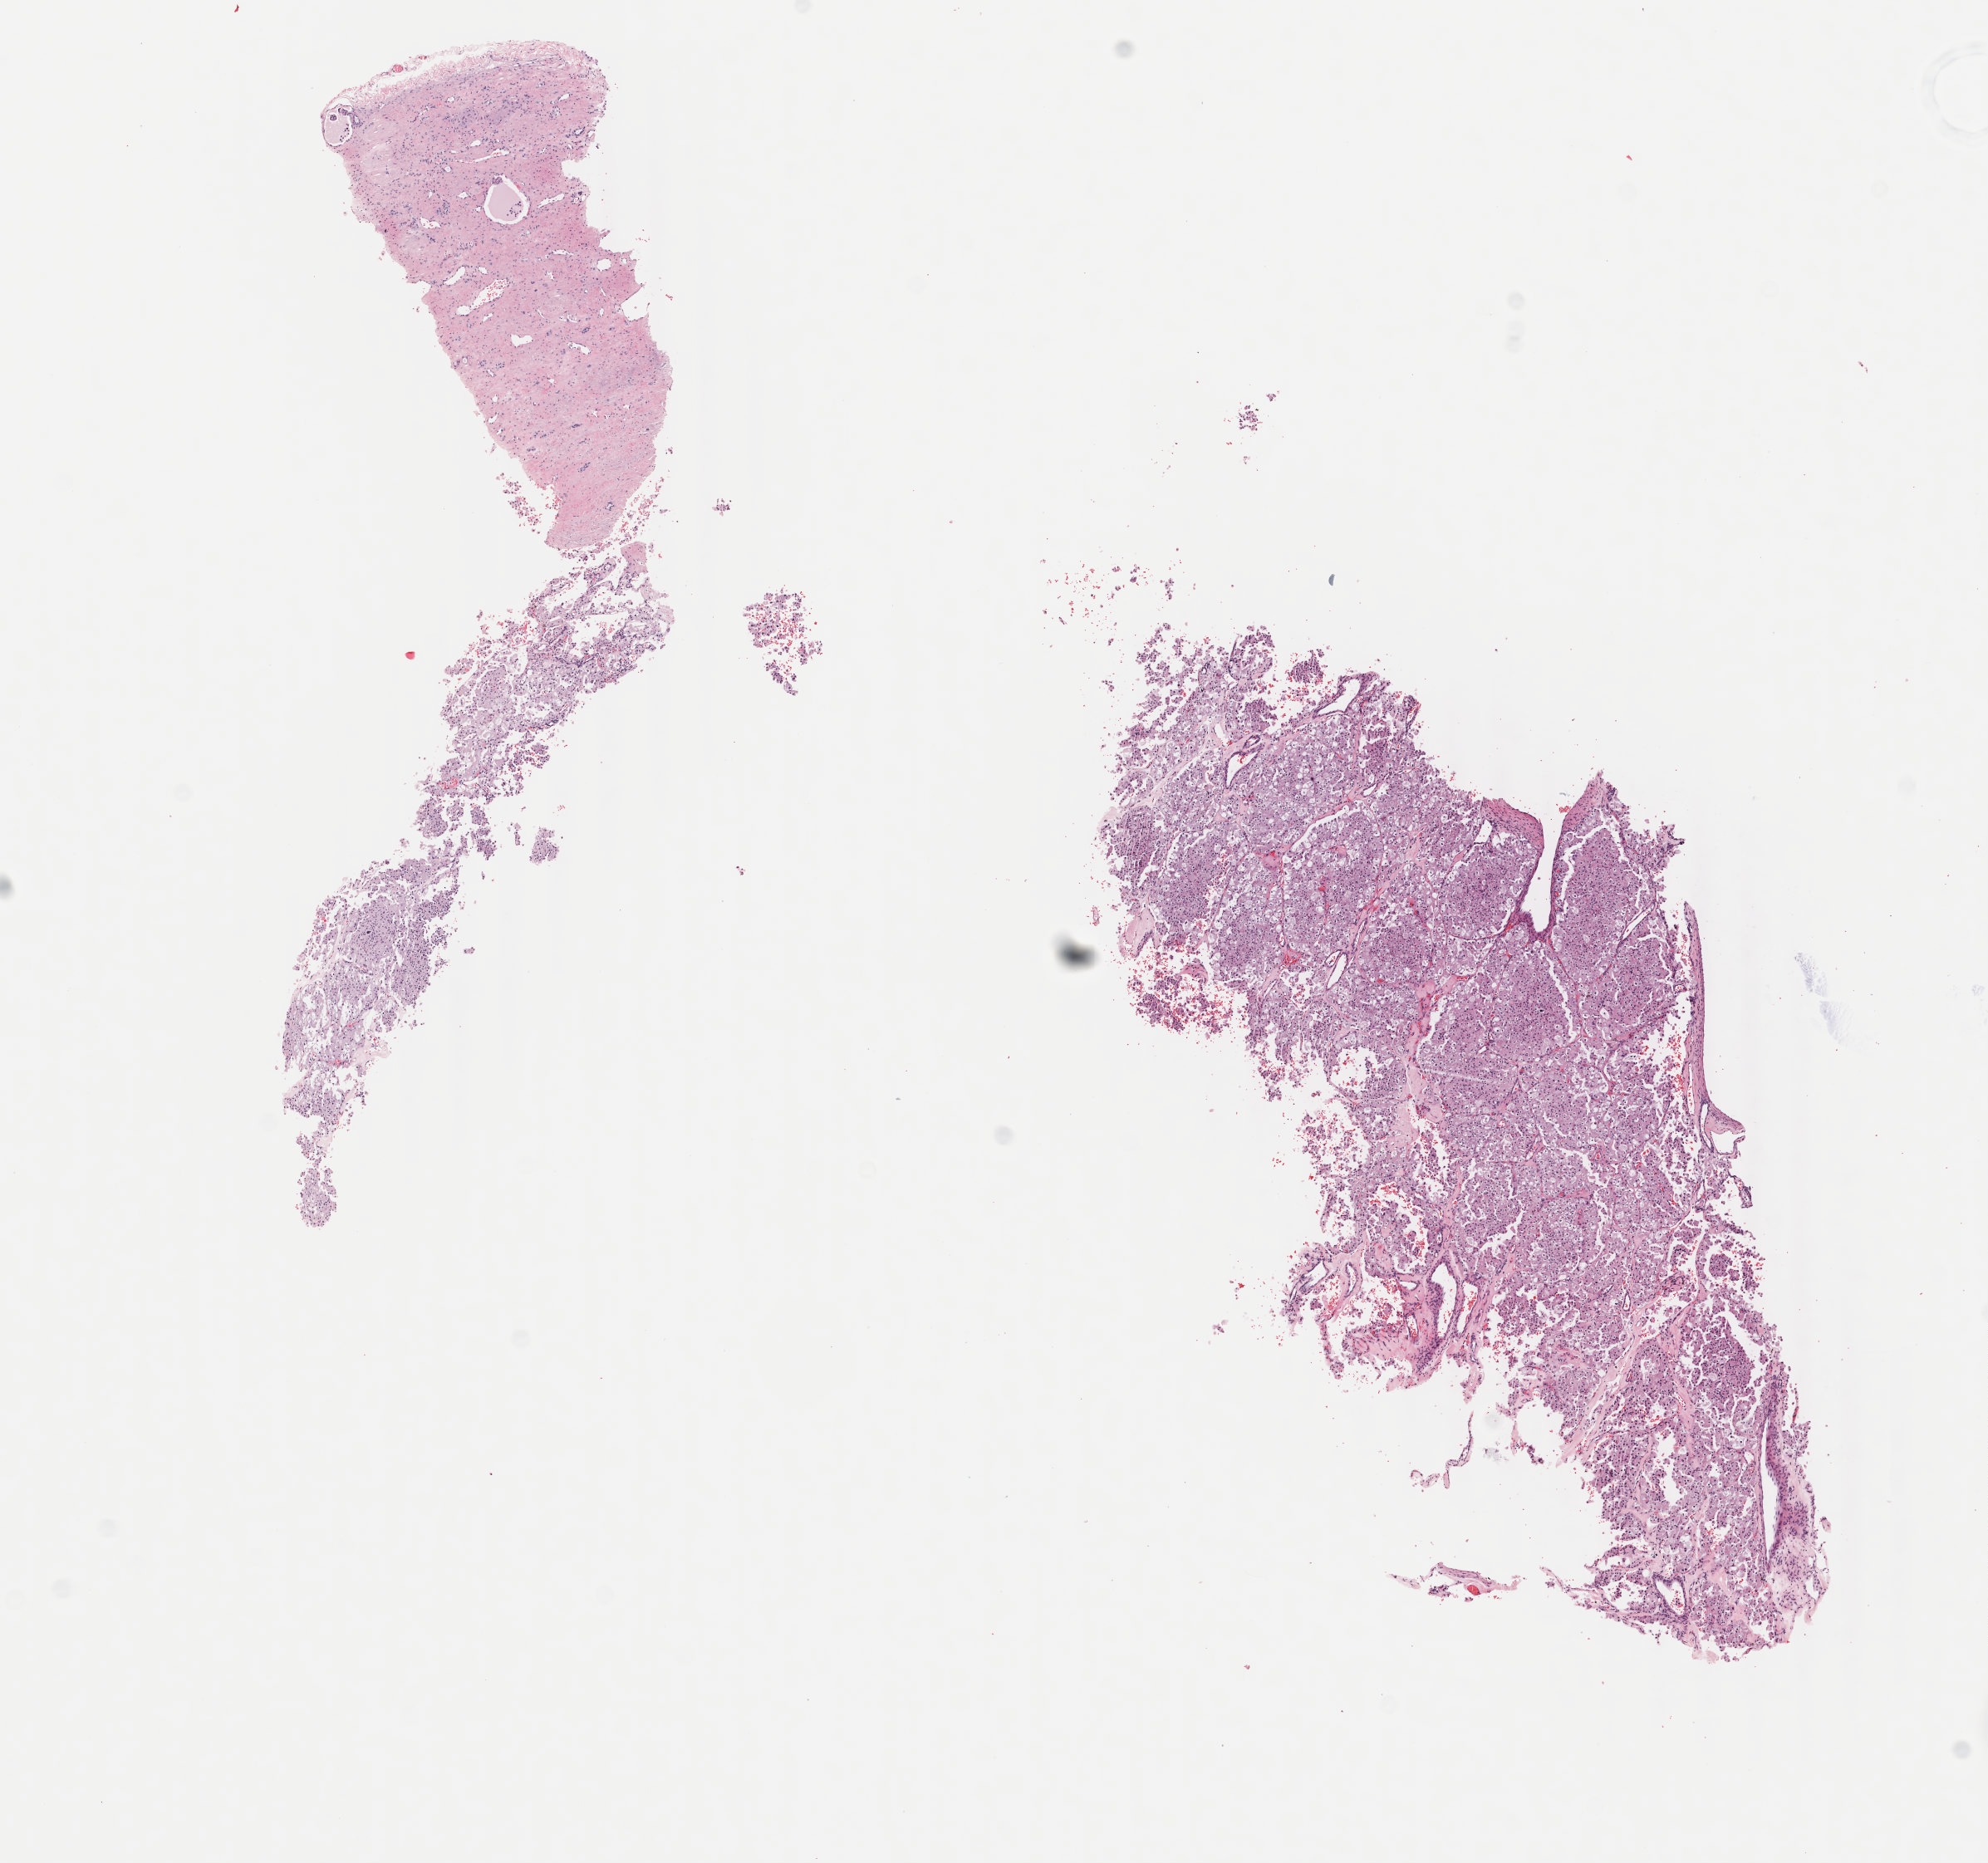
Whole-slide histology image, H&E, a low-resolution overview of the entire scanned area, about 9.5 x 8.9 mm (slide scanned at 40x). Frozen section. Primary tumour sample from the kidney. Male, age 59 years at initial diagnosis. Histologic grade: G2 (moderately differentiated). Composition of this section per pathologist review: tumour cells 70%, tumour nuclei 75%, normal cells 0%, stromal cells 30%, necrosis 0%. Inflammatory infiltration, as recorded: lymphocyte infiltration 1%, monocyte infiltration 1%, neutrophil infiltration 0%.
AJCC pathologic stage: II. Histologic diagnosis: Clear cell adenocarcinoma, NOS. TNM: T2 NX M0.